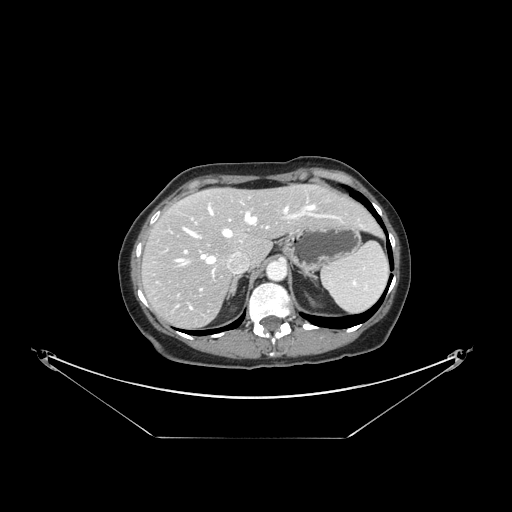
Contrast-enhanced abdominal CT, one axial slice; reconstruction kernel STANDARD; 120 kVp; intravenous contrast given; soft-tissue window (W 400 / L 40 HU); 2.5 mm slice thickness; 512 × 512 image matrix, field of view 500 × 500 mm. Female patient, age 73 years. Case-level facts recorded for this patient, not image findings: diagnosis: colorectal cancer liver metastases, imaged before liver resection; multiple liver metastases: no; largest metastasis: 1 cm; disease in both lobes: no.
Outlined on this slice (outlined manually by an expert reader):
- hepatic veins: box from (x=175, y=204) to (x=359, y=310) px
- liver: (x=143, y=185)–(x=377, y=327)
- planned liver remnant (the part of the liver to remain after resection): (x=168, y=185)–(x=378, y=262)
- portal vein (with intrahepatic branches): (x=184, y=209)–(x=333, y=291)